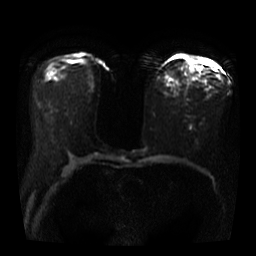
Breast MRI, one axial slice. Slice 19 of 40 in the series (ordered by position). Diffusion-weighted series; image 2 of 4 stored at this slice position (different b-values; order by instance number). 3 T. 5 mm slice thickness. 256 × 256 image matrix, field of view 360 × 360 mm. Female patient.
Structures marked on this image (manually delineated by an expert):
- tumour on diffusion-weighted imaging: bounding box (x1, y1, x2, y2) in pixels: (187, 63, 196, 73)